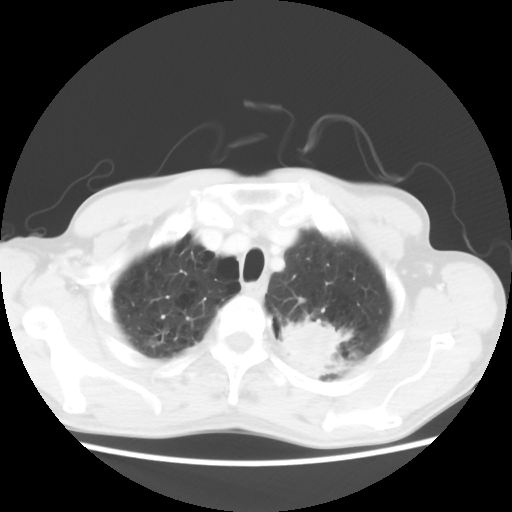
Chest CT, one axial slice. Position 55 of 64 along the scan axis. Reconstruction kernel STANDARD. Lung window (W 1500 / L -600 HU). 5 mm slice thickness. 512 × 512 image matrix, field of view 346 × 346 mm. Male patient, age 63 years. From the clinical record (not read from this slice): clinical TNM (as recorded): T2 N0 M0.
Outlined on this slice (rectangle marked by the reading radiologist):
- lung tumour (recorded histology: adenocarcinoma): bounding box <275,312,352,391> (left, top, right, bottom; pixels)